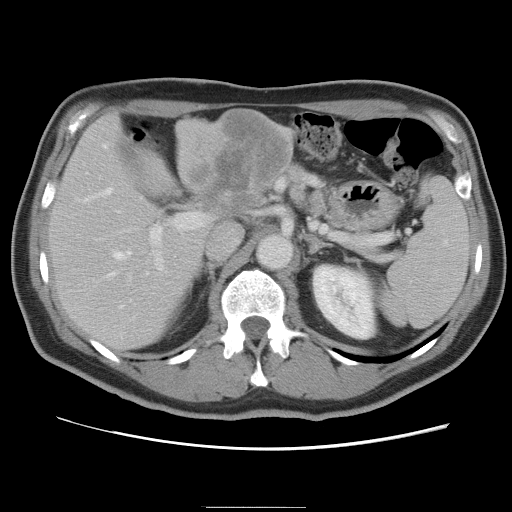
Contrast-enhanced abdominal CT, one axial slice. 120 kVp. Intravenous contrast given. Soft-tissue window (W 400 / L 40 HU). 5 mm slice thickness. 512 × 512 image matrix, field of view 363 × 363 mm. Male patient, age 63 years. Case-level facts recorded for this patient, not image findings: diagnosis: colorectal cancer liver metastases, imaged before liver resection; multiple liver metastases: no; largest metastasis: 9 cm; disease in both lobes: no.
Annotated regions visible in this slice (outlined manually by an expert reader):
- hepatic veins: box from (x=95, y=144) to (x=149, y=309) px
- liver: (x=49, y=109)–(x=294, y=354)
- planned liver remnant (the part of the liver to remain after resection): (x=50, y=146)–(x=205, y=354)
- portal vein (with intrahepatic branches): (x=117, y=210)–(x=208, y=281)
- liver metastasis: (x=189, y=115)–(x=284, y=218)